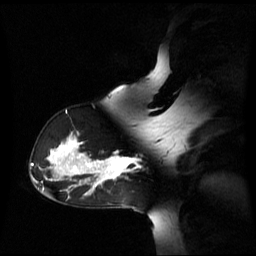
Breast MRI (dynamic contrast-enhanced), one sagittal slice. Slice 42 of 60 in the series (ordered by position). Dynamic contrast-enhanced series, image 2 of 3 at this slice position (ordered by acquisition). 1.5 T. TE 4.2 ms, TR 8.4 ms. 256 × 256 image matrix. Female patient, age 39 years. From the clinical record (not read from this slice): setting: breast cancer imaged before/during neoadjuvant chemotherapy; receptor status: triple-negative.
Structures marked on this image (semi-automatic segmentation, software-assisted and operator-edited):
- analysis volume of interest (the breast-tissue region the enhancement analysis was run in; not a lesion): bounding box [x1, y1, x2, y2] px = [105, 156, 140, 179]
- tumour enhancement mask (voxels above the 70 % enhancement threshold inside the analysis volume of interest): [105, 156, 138, 179]